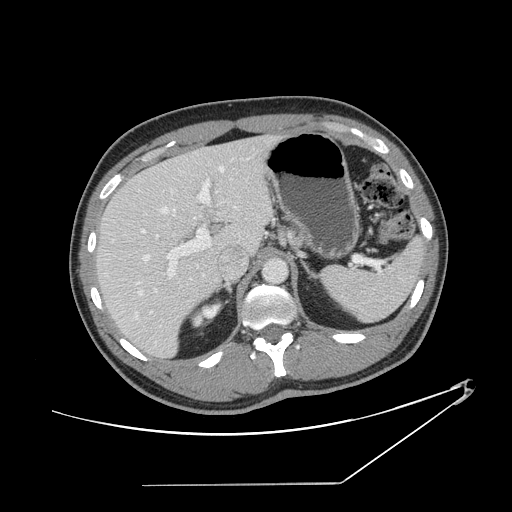
Contrast-enhanced abdominal CT, one axial slice. Slice 93 of 152 in the series (ordered by position). Intravenous contrast given. Soft-tissue window (W 400 / L 40 HU). 2.5 mm slice thickness. 512 × 512 image matrix, field of view 432 × 432 mm. Male patient, age 45 years. From the clinical record (not read from this slice): diagnosis: colorectal cancer liver metastases, imaged before liver resection; multiple liver metastases: no; largest metastasis: 1 cm; disease in both lobes: no.
Outlined on this slice (manually delineated by an expert):
- hepatic veins: bounding box <111,159,237,296> (left, top, right, bottom; pixels)
- liver: <98,137,272,357>
- planned liver remnant (the part of the liver to remain after resection): <98,155,227,357>
- portal vein (with intrahepatic branches): <141,180,211,314>